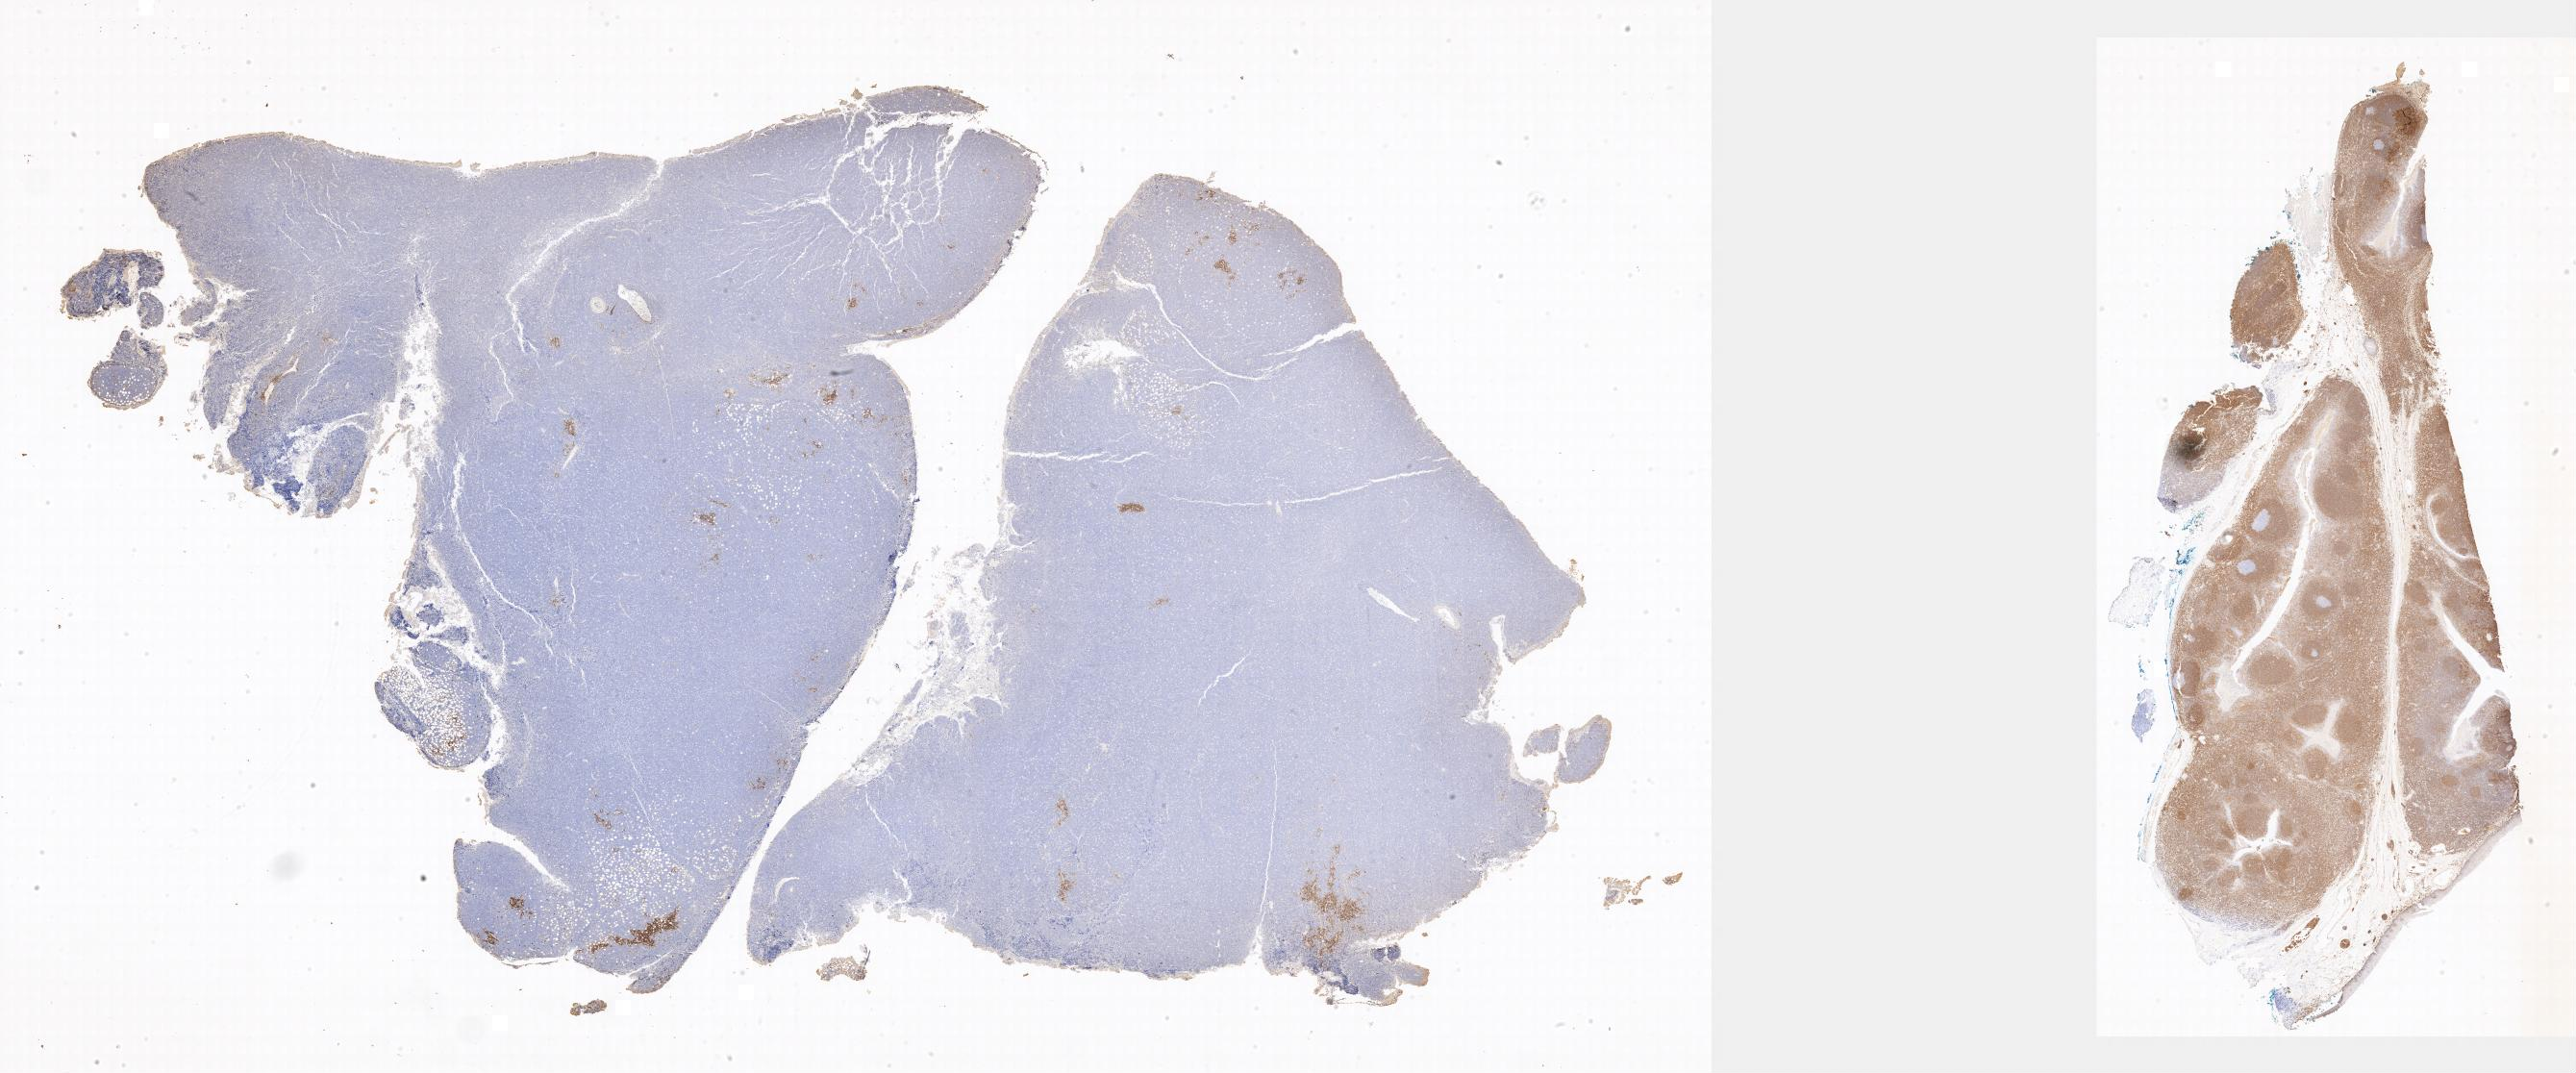
Whole-slide image, immunohistochemical stain for BCL2 — low-resolution overview of the scanned area; specimen: tumor tissue; anatomic site: peritoneum. Male patient; age at initial diagnosis 9 years.
Histologic diagnosis: Burkitt lymphoma, NOS.